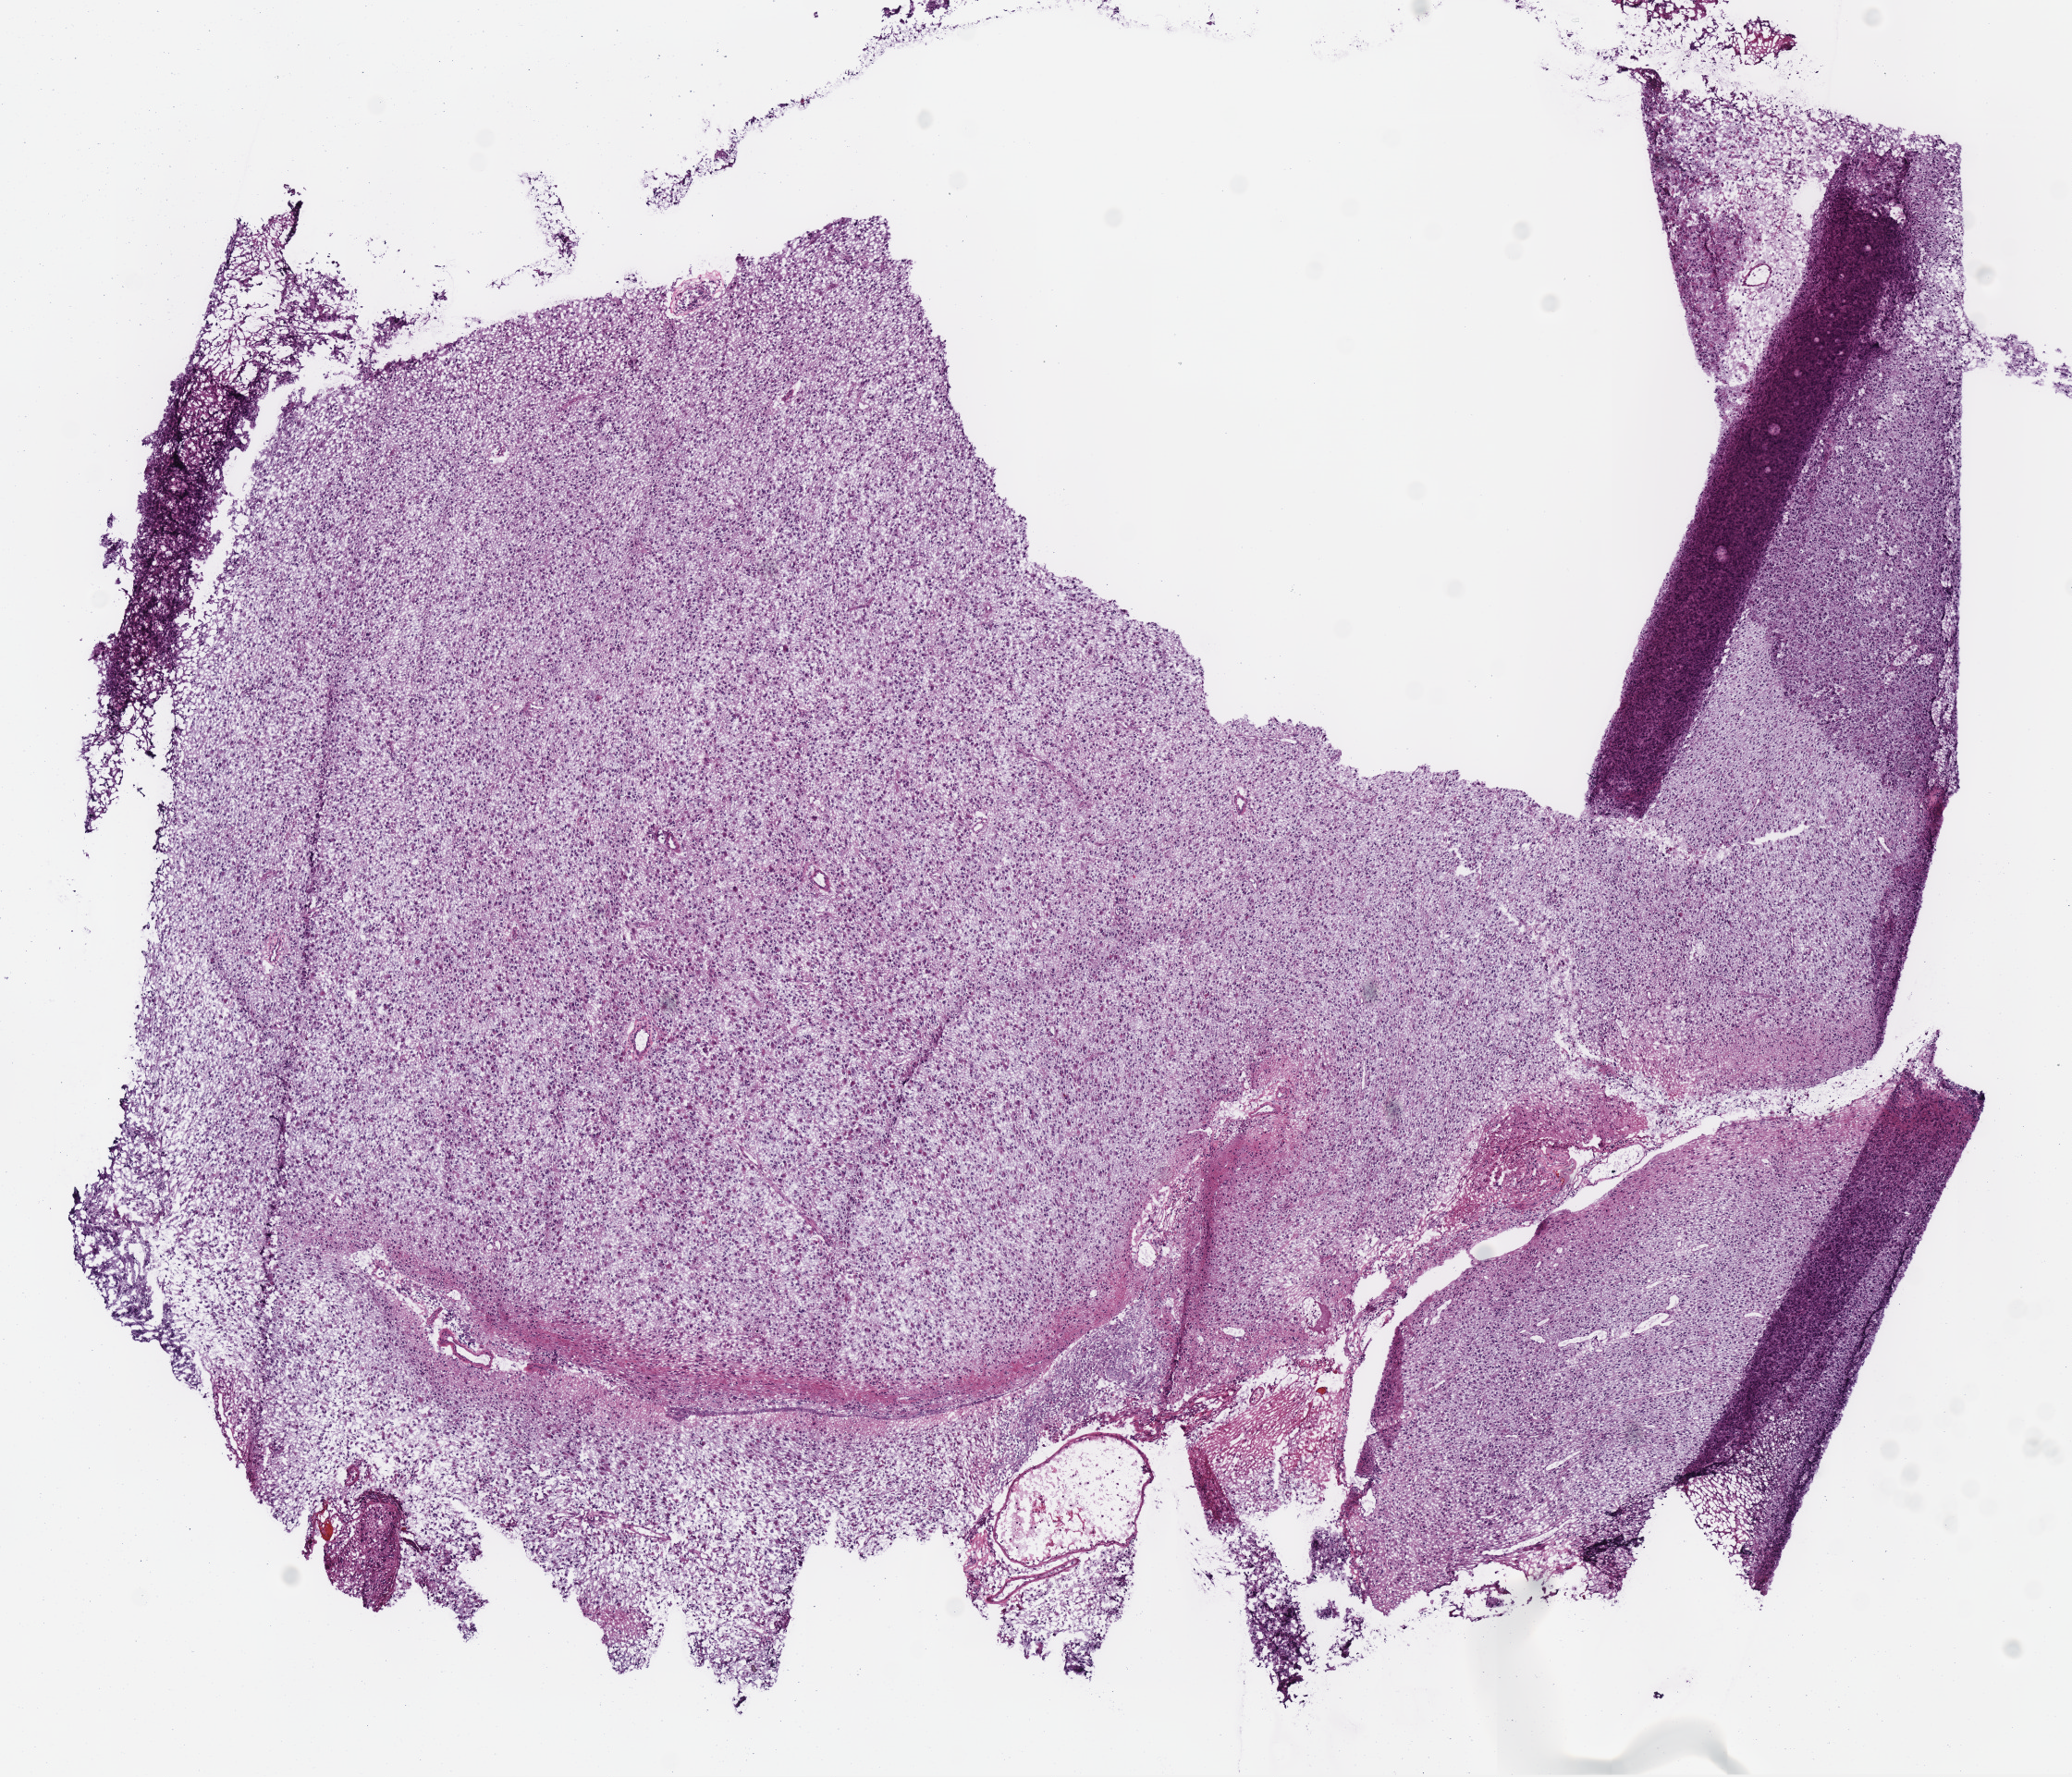
Digitized H&E-stained tissue section (whole slide), low-resolution overview of the scanned area, about 8.8 x 7.6 mm (from a 40x scan). Frozen section from the bottom of the tissue portion. Primary tumour sample from the brain. Male, age 36 years at initial diagnosis. Histologic grade: G3 (poorly differentiated). Pathologist review of this section (percent, as recorded): tumour cells 100%, tumour nuclei 80%, normal cells 0%, stromal cells 0%, necrosis 0%.
* pathologic diagnosis: Mixed glioma (cerebrum)